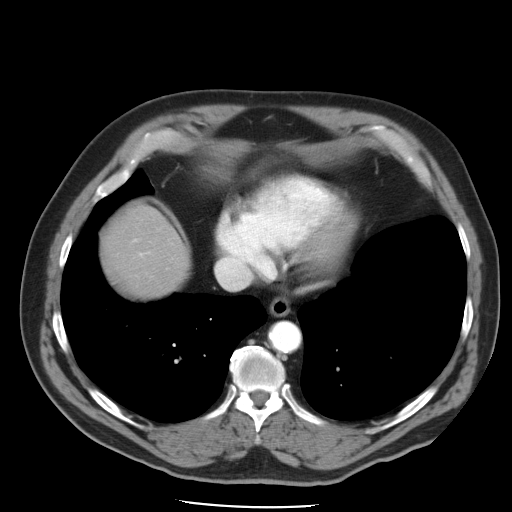
Contrast-enhanced abdominal CT, one axial slice; position 44 of 49 along the scan axis; 120 kVp; soft-tissue window (W 400 / L 40 HU); 5 mm slice thickness; 512 × 512 image matrix, field of view 395 × 395 mm. Male patient, age 68 years. Case-level facts recorded for this patient, not image findings: diagnosis: colorectal cancer liver metastases, imaged before liver resection; multiple liver metastases: yes.
Structures marked on this image (manually delineated by an expert):
- hepatic veins: bounding box (x1, y1, x2, y2) in pixels: (216, 254, 251, 290)
- liver: (105, 208, 189, 293)
- planned liver remnant (the part of the liver to remain after resection): (105, 208, 189, 294)